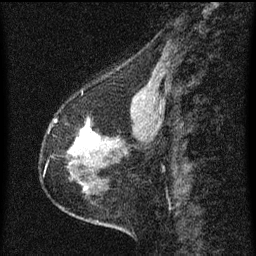
Breast MRI (dynamic contrast-enhanced), one sagittal slice; position 25 of 60 along the scan axis; dynamic contrast-enhanced series, image 2 of 3 at this slice position (ordered by acquisition); 1.5 T; TE 4.2 ms, TR 8 ms; 2 mm slice thickness; 256 × 256 image matrix, field of view 180 × 180 mm. Female patient, age 56 years.
Annotated regions visible in this slice (semi-automatically segmented with operator editing):
- analysis volume of interest (the breast-tissue region the enhancement analysis was run in; not a lesion): bounding box <64,115,102,181> (left, top, right, bottom; pixels)
- tumour enhancement mask (voxels above the 70 % enhancement threshold inside the analysis volume of interest): <75,127,95,147>